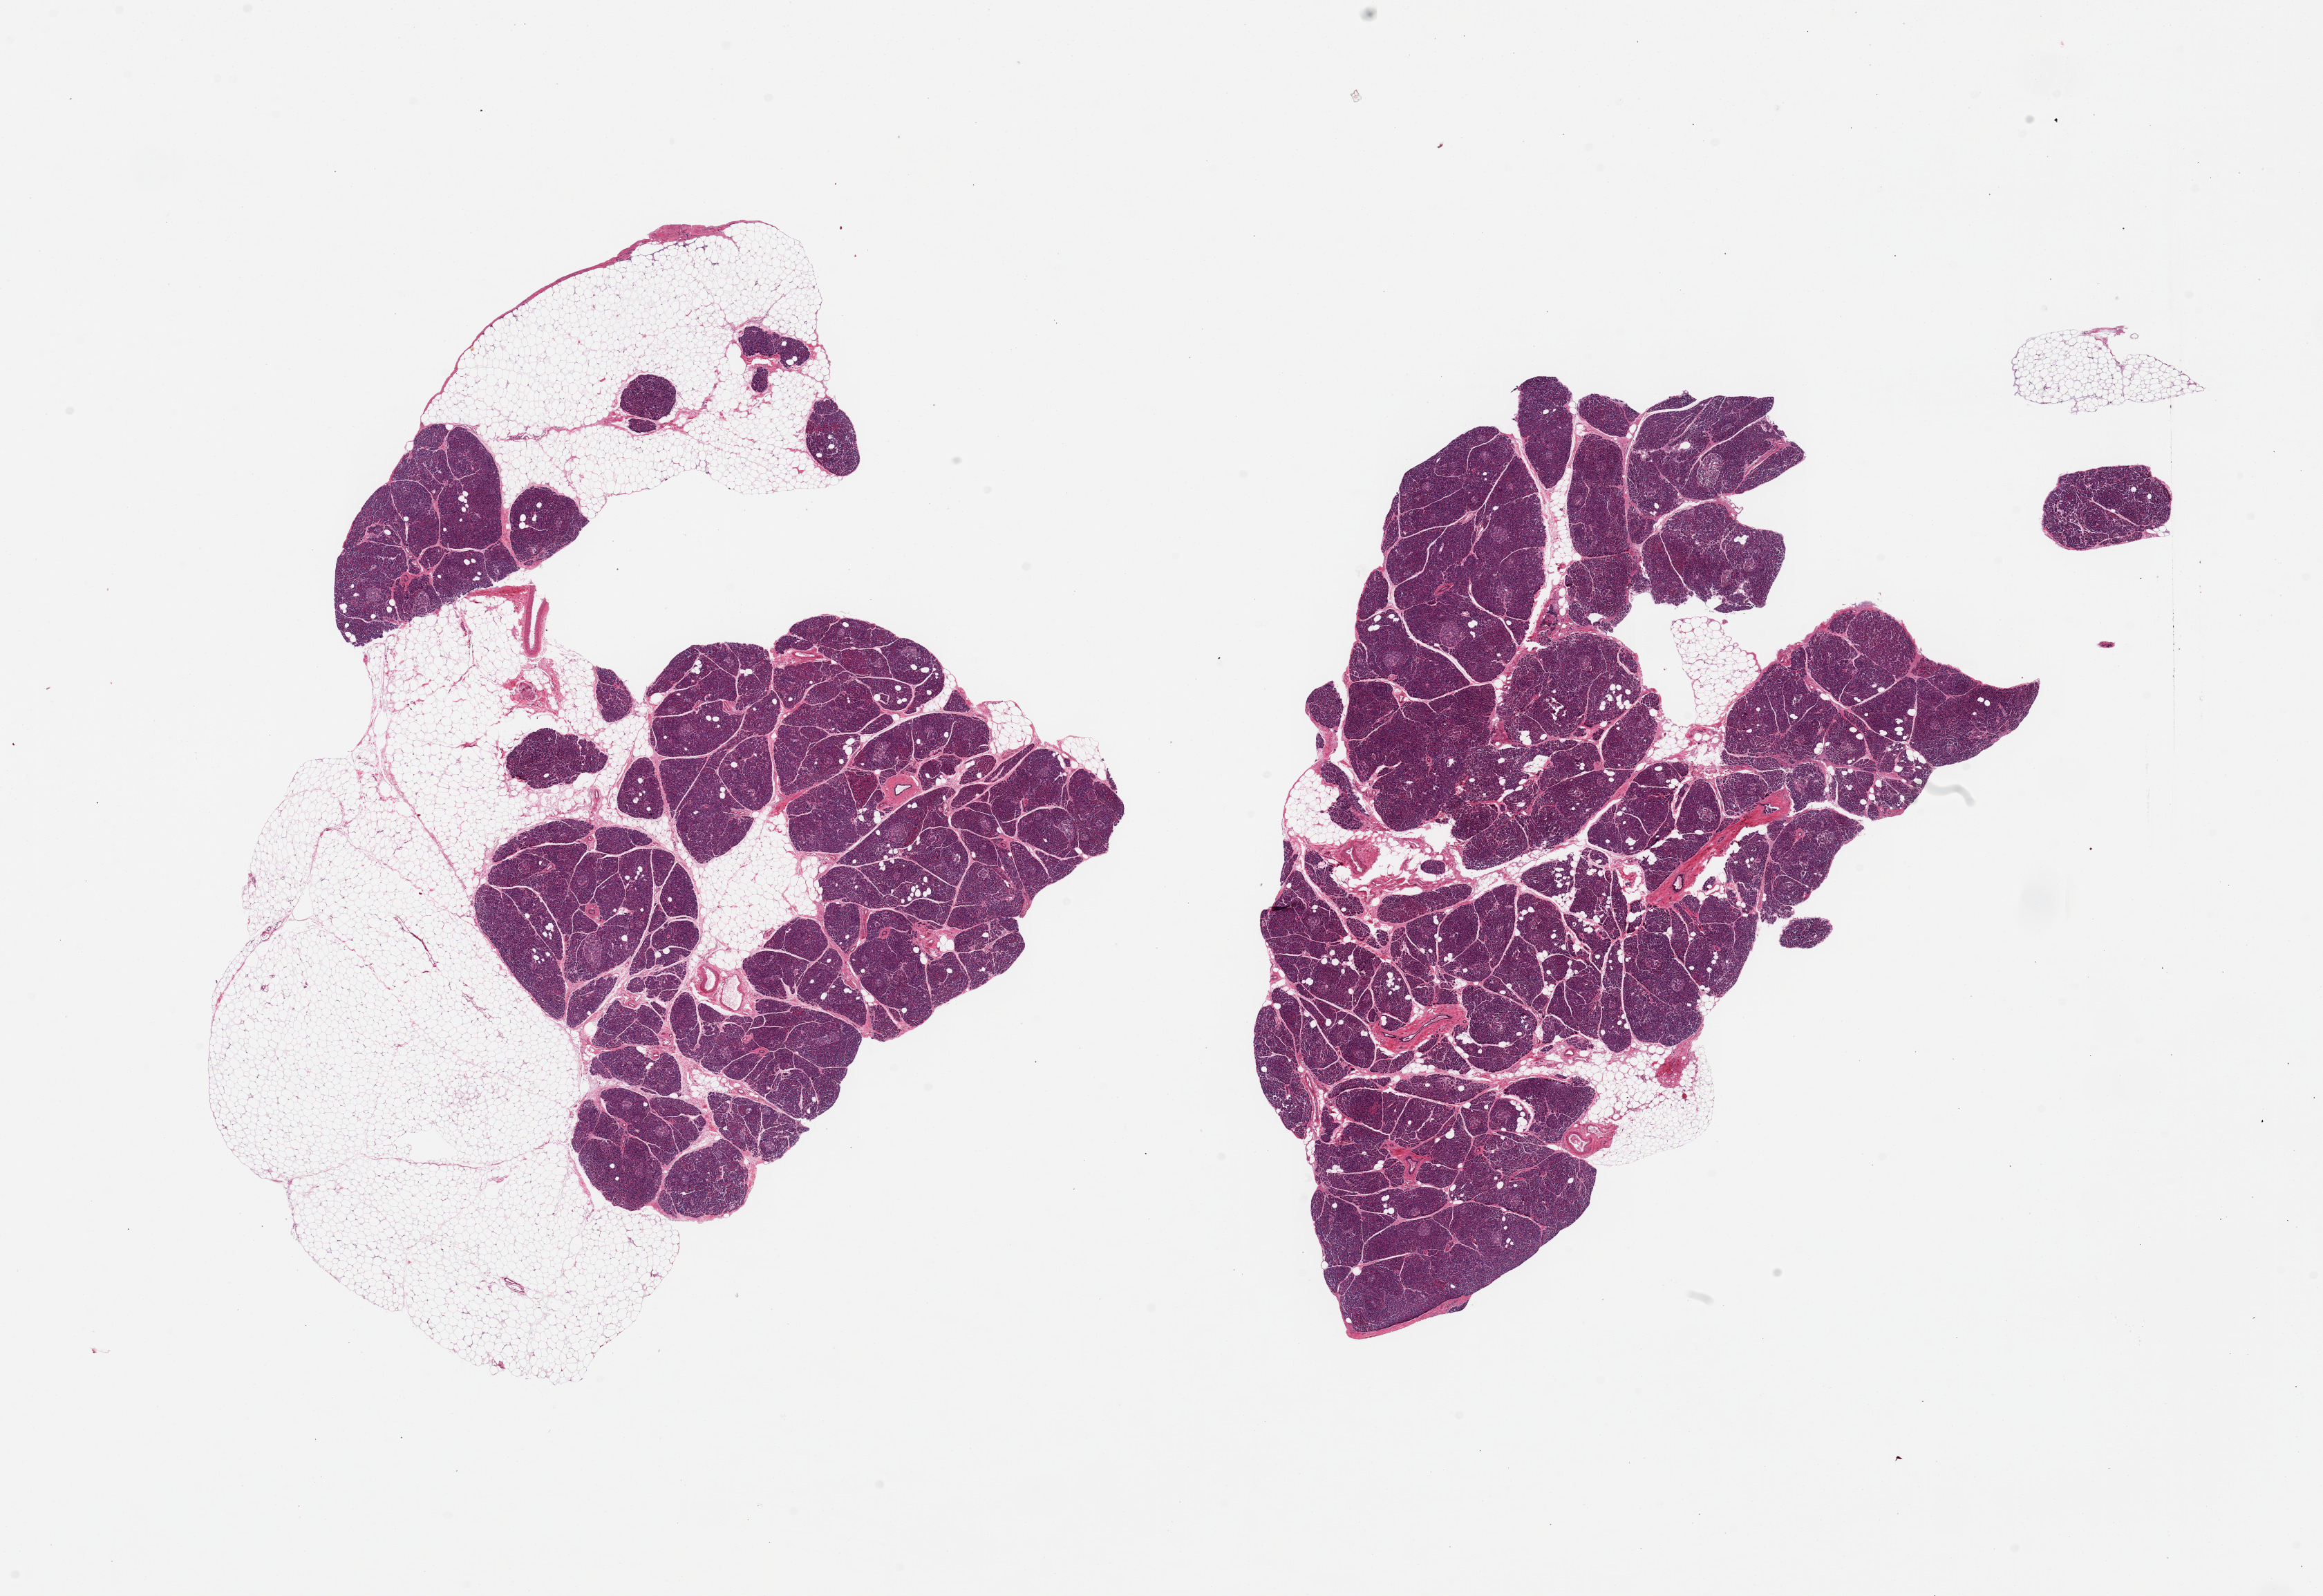
Haematoxylin and eosin whole-slide image, whole scanned area (about 26.6 x 18.3 mm) shown as a low-resolution overview. PAXgene-fixed, paraffin-embedded tissue. Section of pancreas (target tissue). Donor tissue sample. Donor: male.
Pathologist's review note for this sample: 2 pieces; 1 piece is ~50% fat, 2nd includes only minor proportion of fat.